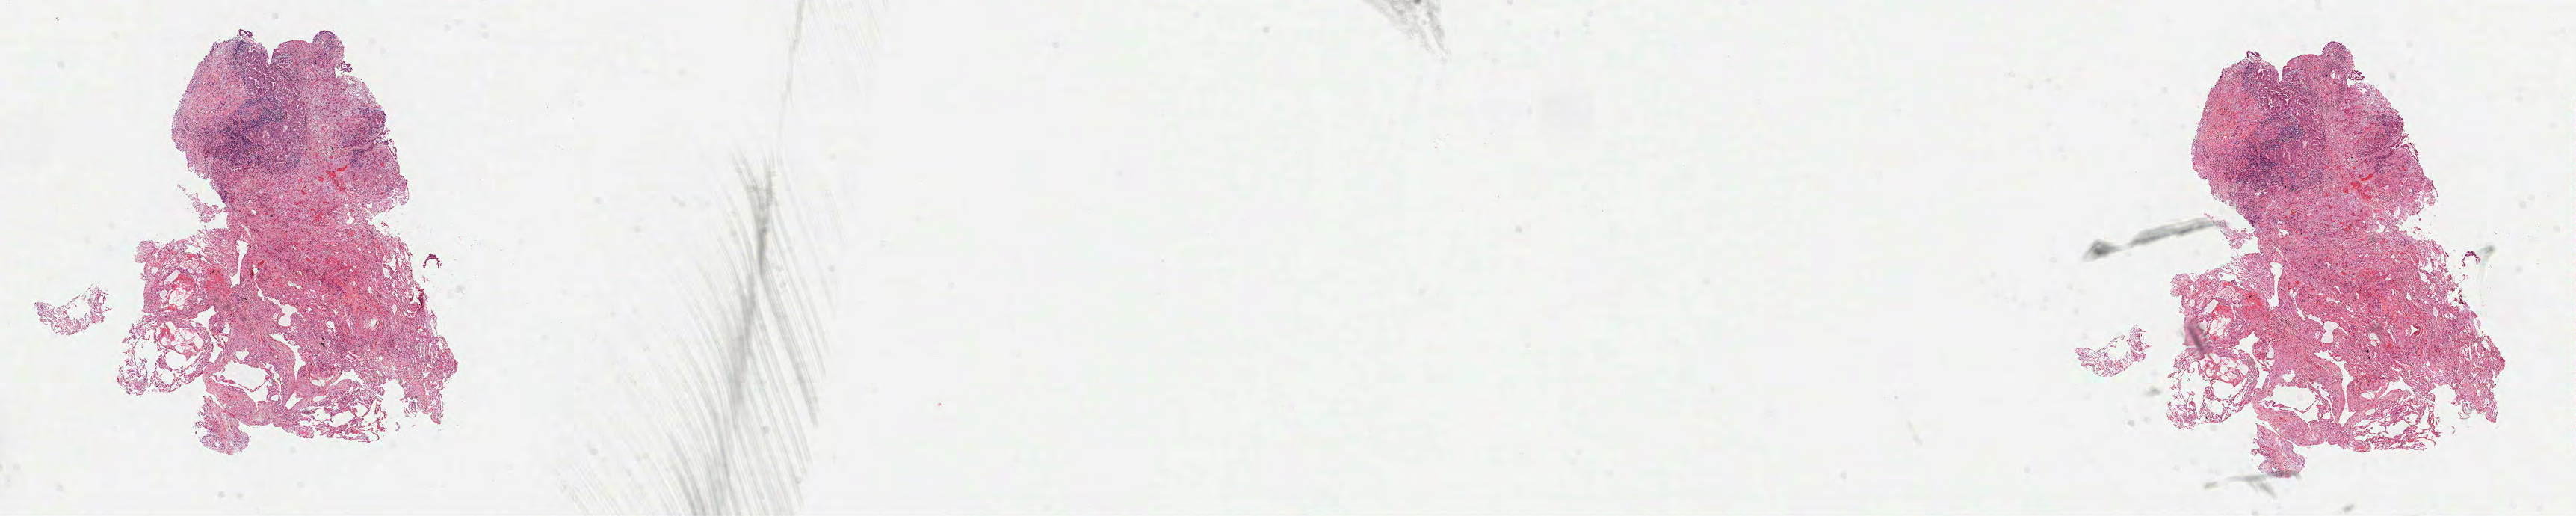
Digitized Hematoxylin and eosin (H&E) stained tissue section (whole slide), whole scanned area (about 27.8 x 5.6 mm, acquisition: 40x scan) shown as a low-resolution overview. Formalin-fixed paraffin-embedded (FFPE) diagnostic section. Lung, primary tumour sample. Female, age 65 years at initial diagnosis.
• AJCC pathologic stage: IA (6th edition)
• pathologic diagnosis: Adenocarcinoma, NOS